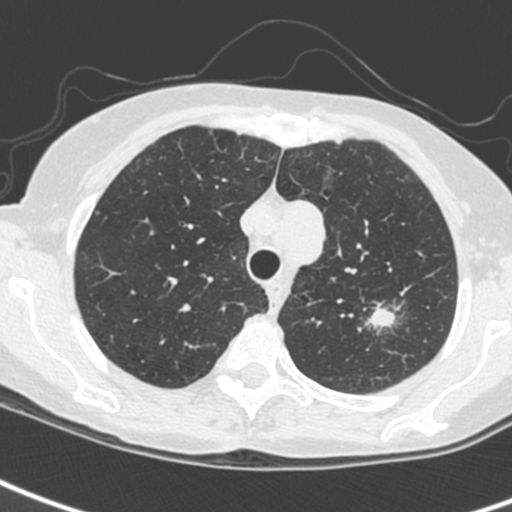
Chest CT (low-dose screening protocol), one axial image; baseline screening round; lung window (W 1500 / L -600 HU); 1.3 mm slice thickness; standard (soft-tissue) reconstruction kernel (C). Female participant, aged 61 years at enrolment. Current smoker at enrolment.
Expert-annotated lung lesion, bounding box (x1, y1, x2, y2) in pixels: (347, 295, 412, 348). The screening reader recorded 2 non-calcified nodules or masses ≥4 mm on this exam (left upper lobe, left upper lobe); which of them this box marks is not recorded. Lung cancer was diagnosed 29 days after this screen: small cell carcinoma, NOS, left upper lobe, stage IV (AJCC 6th edition).